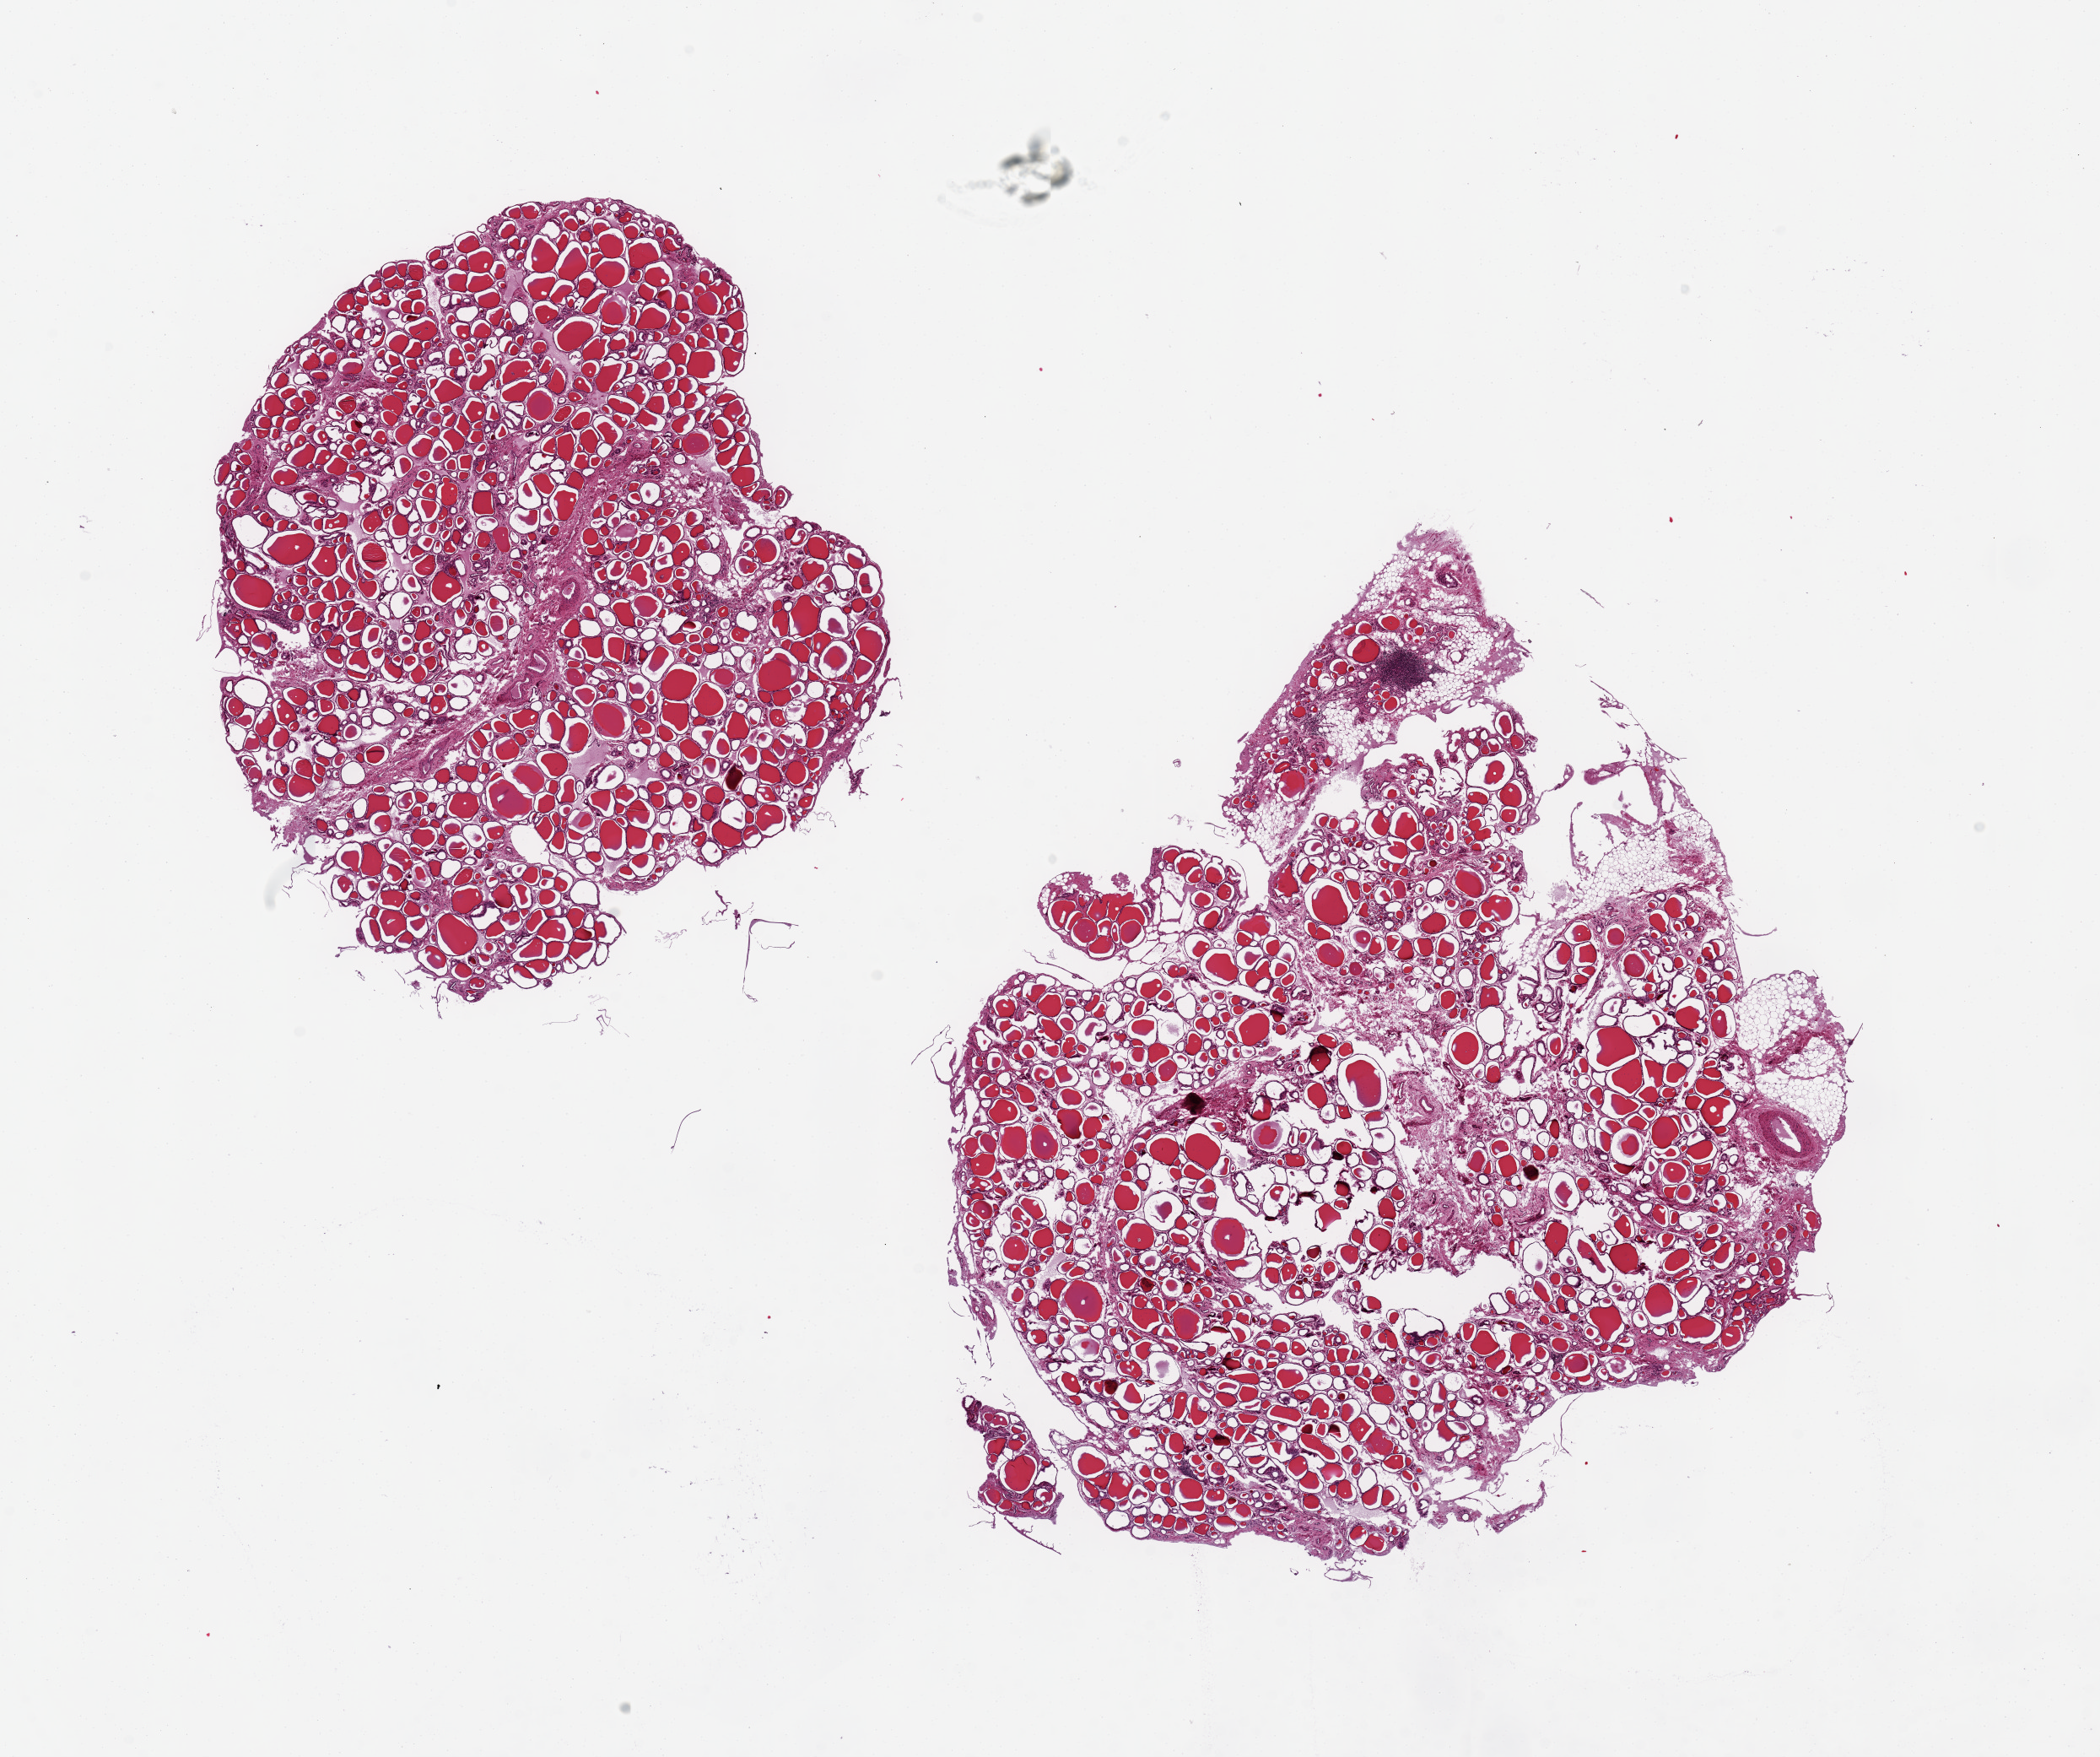
Whole-slide image, H&E stain, whole scanned area (about 19.7 x 16.5 mm, slide scanned at 20x) shown as a low-resolution overview, PAXgene-fixed paraffin-embedded (PFPE) section, sampled site (target tissue): thyroid, donor tissue sample. Donor sex: male.
- review note (as recorded): 2 ~9x7mm aliquots, patchy areas of regression/fibrosis